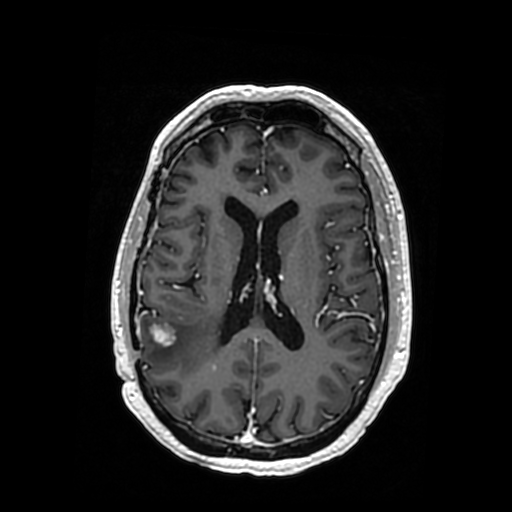
Brain MRI from a brain-tumour surgery series, one axial slice; slice 157 of 364 in the series (ordered by position); T1-weighted post-contrast; 512 × 512 image matrix, field of view 260 × 260 mm. From the clinical record (not read from this slice): histopathology: Oligodendroglioma; WHO grade: 3; IDH mutation: yes; tumour location: Right Posterior Temporal Inferior Parietal.
Annotated regions visible in this slice (manually delineated by an expert):
- tumour: bounding box [x1, y1, x2, y2] px = [146, 323, 217, 371]